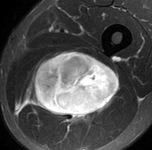
MRI of an extremity soft-tissue mass, one axial slice. Position 68 of 90 along the scan axis. STIR. MR volume resampled by the dataset authors to the PET/CT grid (not the native acquisition matrix). 3.27 mm slice thickness. 152 × 150 image matrix. Male patient. From the clinical record (not read from this slice): histological type: undifferentiated pleomorphic liposarcoma; grade: high; site of the primary tumour: left thigh.
Structures marked on this image (expert contour drawn on MRI and transferred to this co-registered scan by the dataset authors):
- gross tumour volume including surrounding oedema: bounding box [x1, y1, x2, y2] px = [20, 51, 119, 127]
- gross tumour volume (mass): [29, 51, 119, 117]